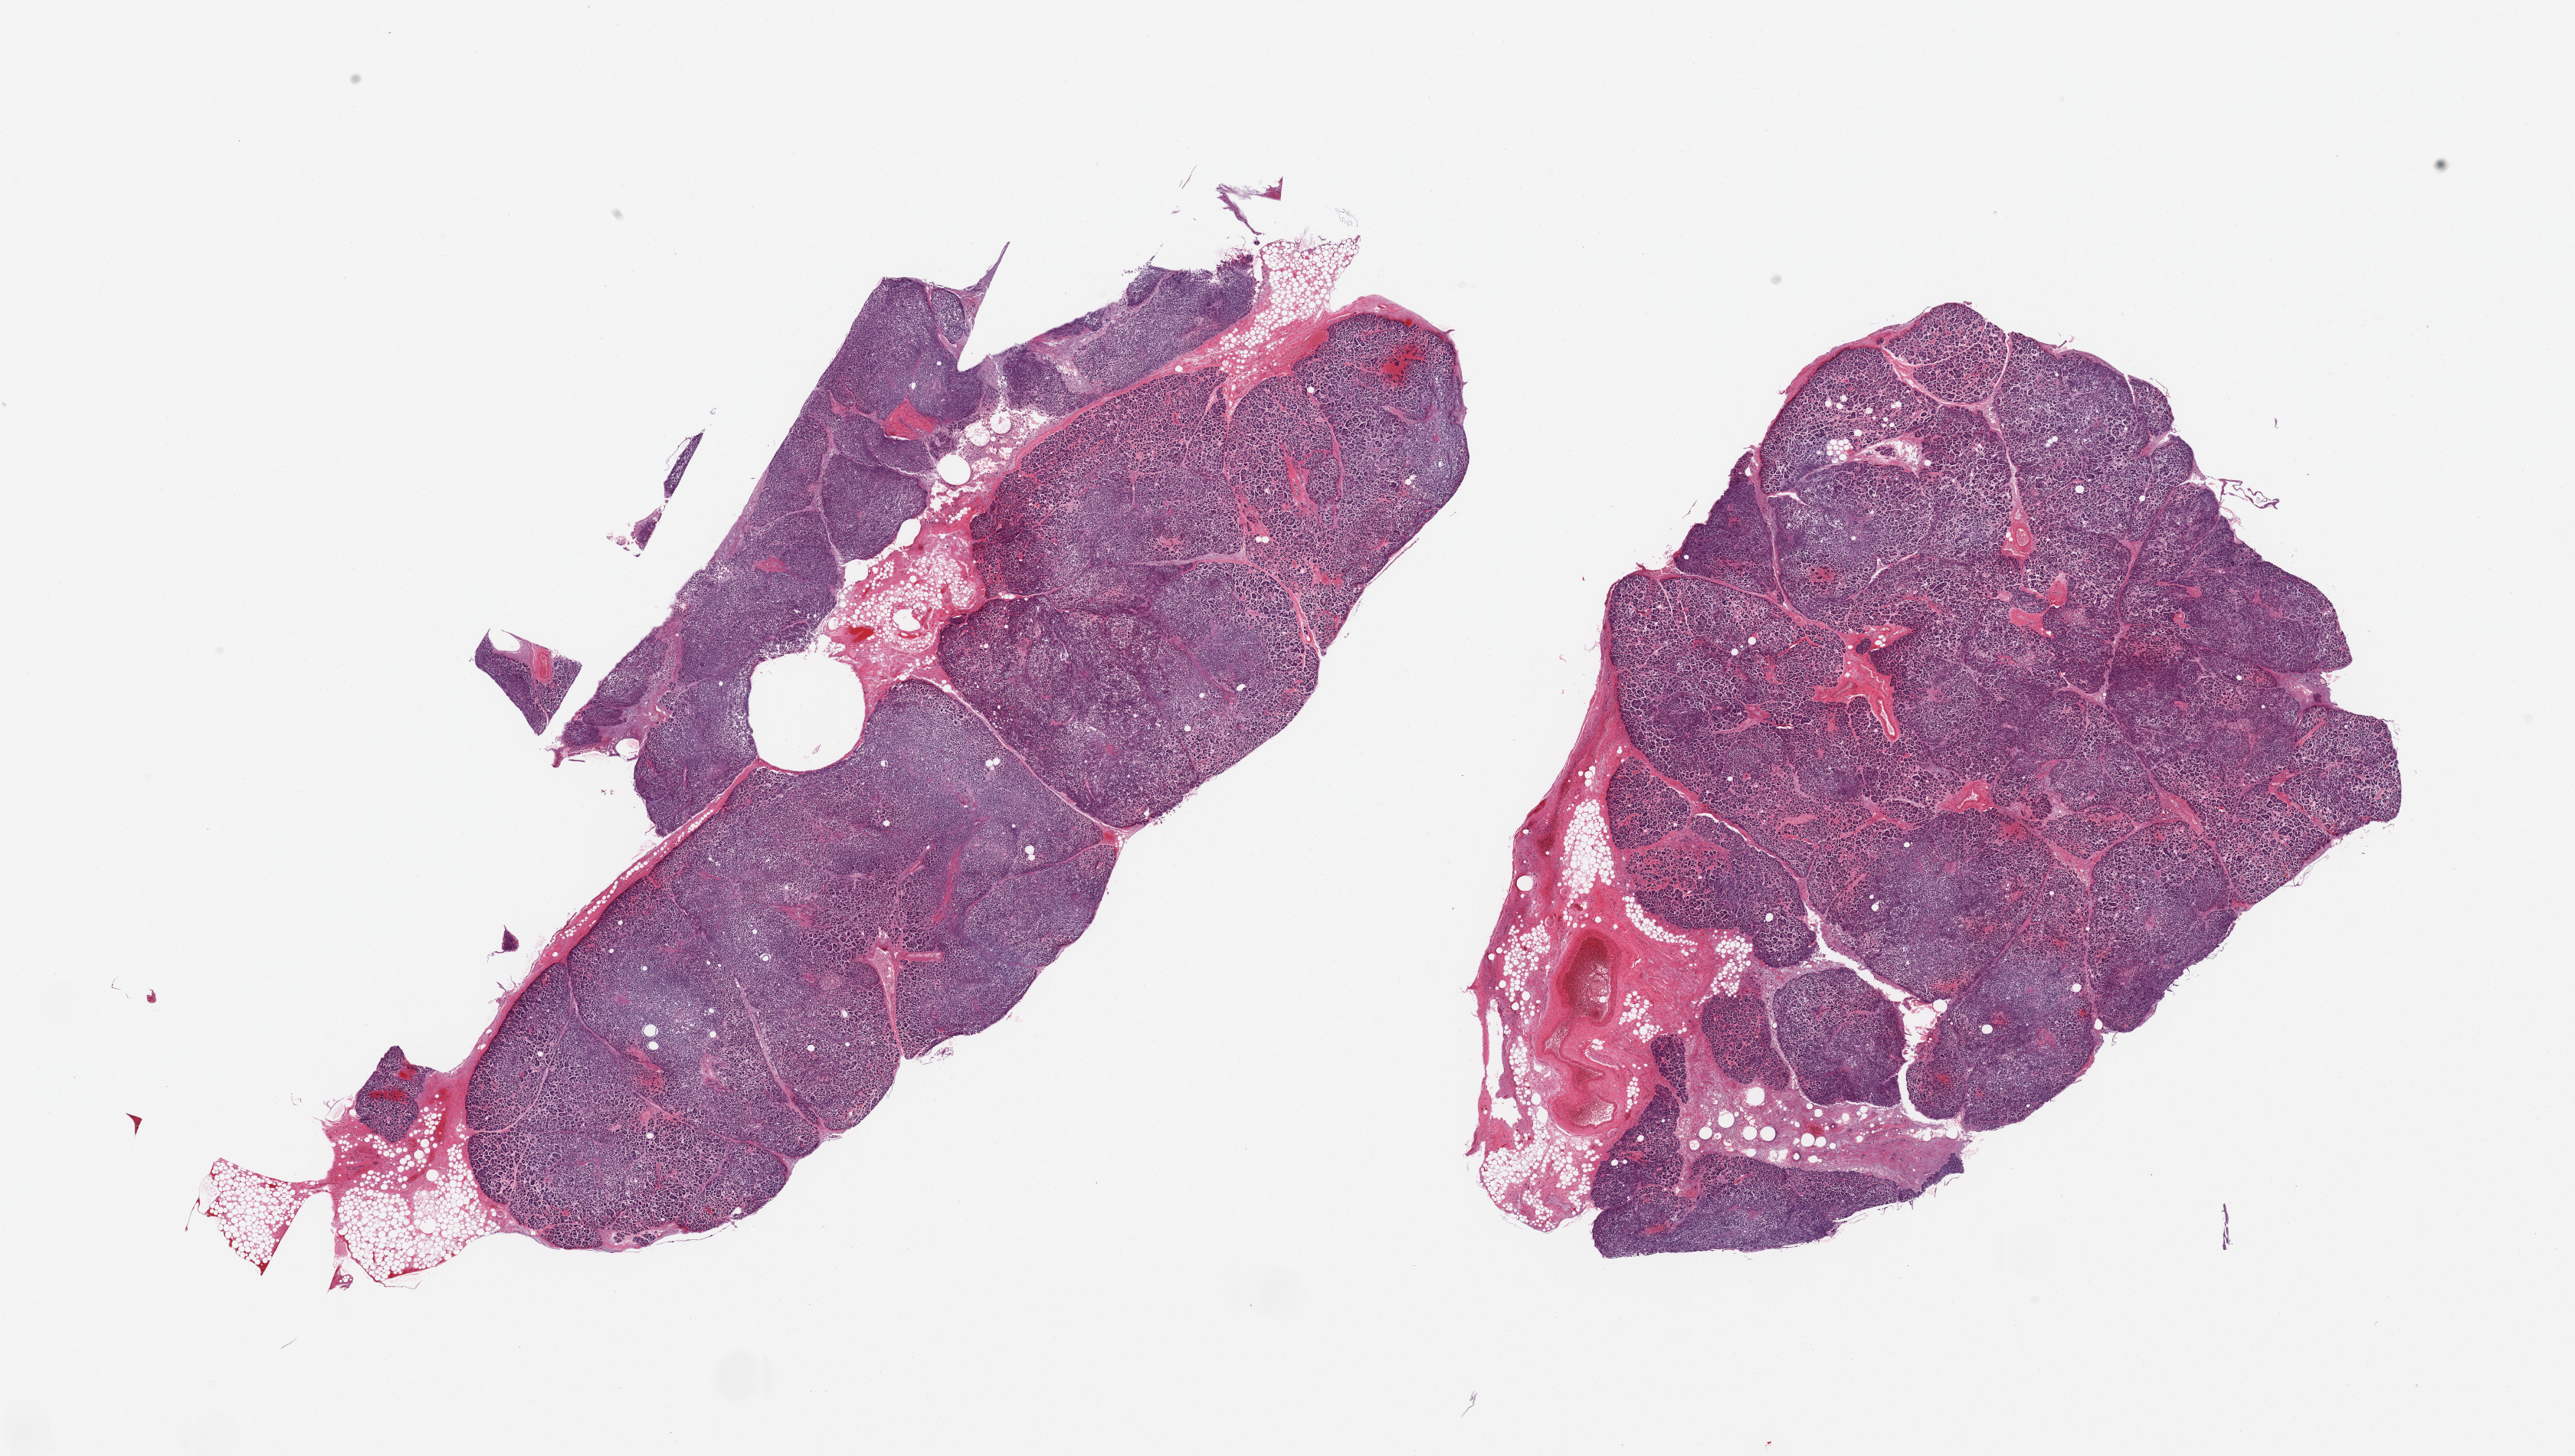
Whole-slide image, haematoxylin and eosin stain, brightfield, a low-resolution overview of the entire scanned area, about 26.6 x 15.0 mm (slide scanned at 20x), PAXgene-fixed, paraffin-embedded tissue, section of pancreas (target tissue), donor tissue sample. Donor: male.
* review note (as recorded): 2 pieces; autolysis varies from moderate to severe; 10% fat content